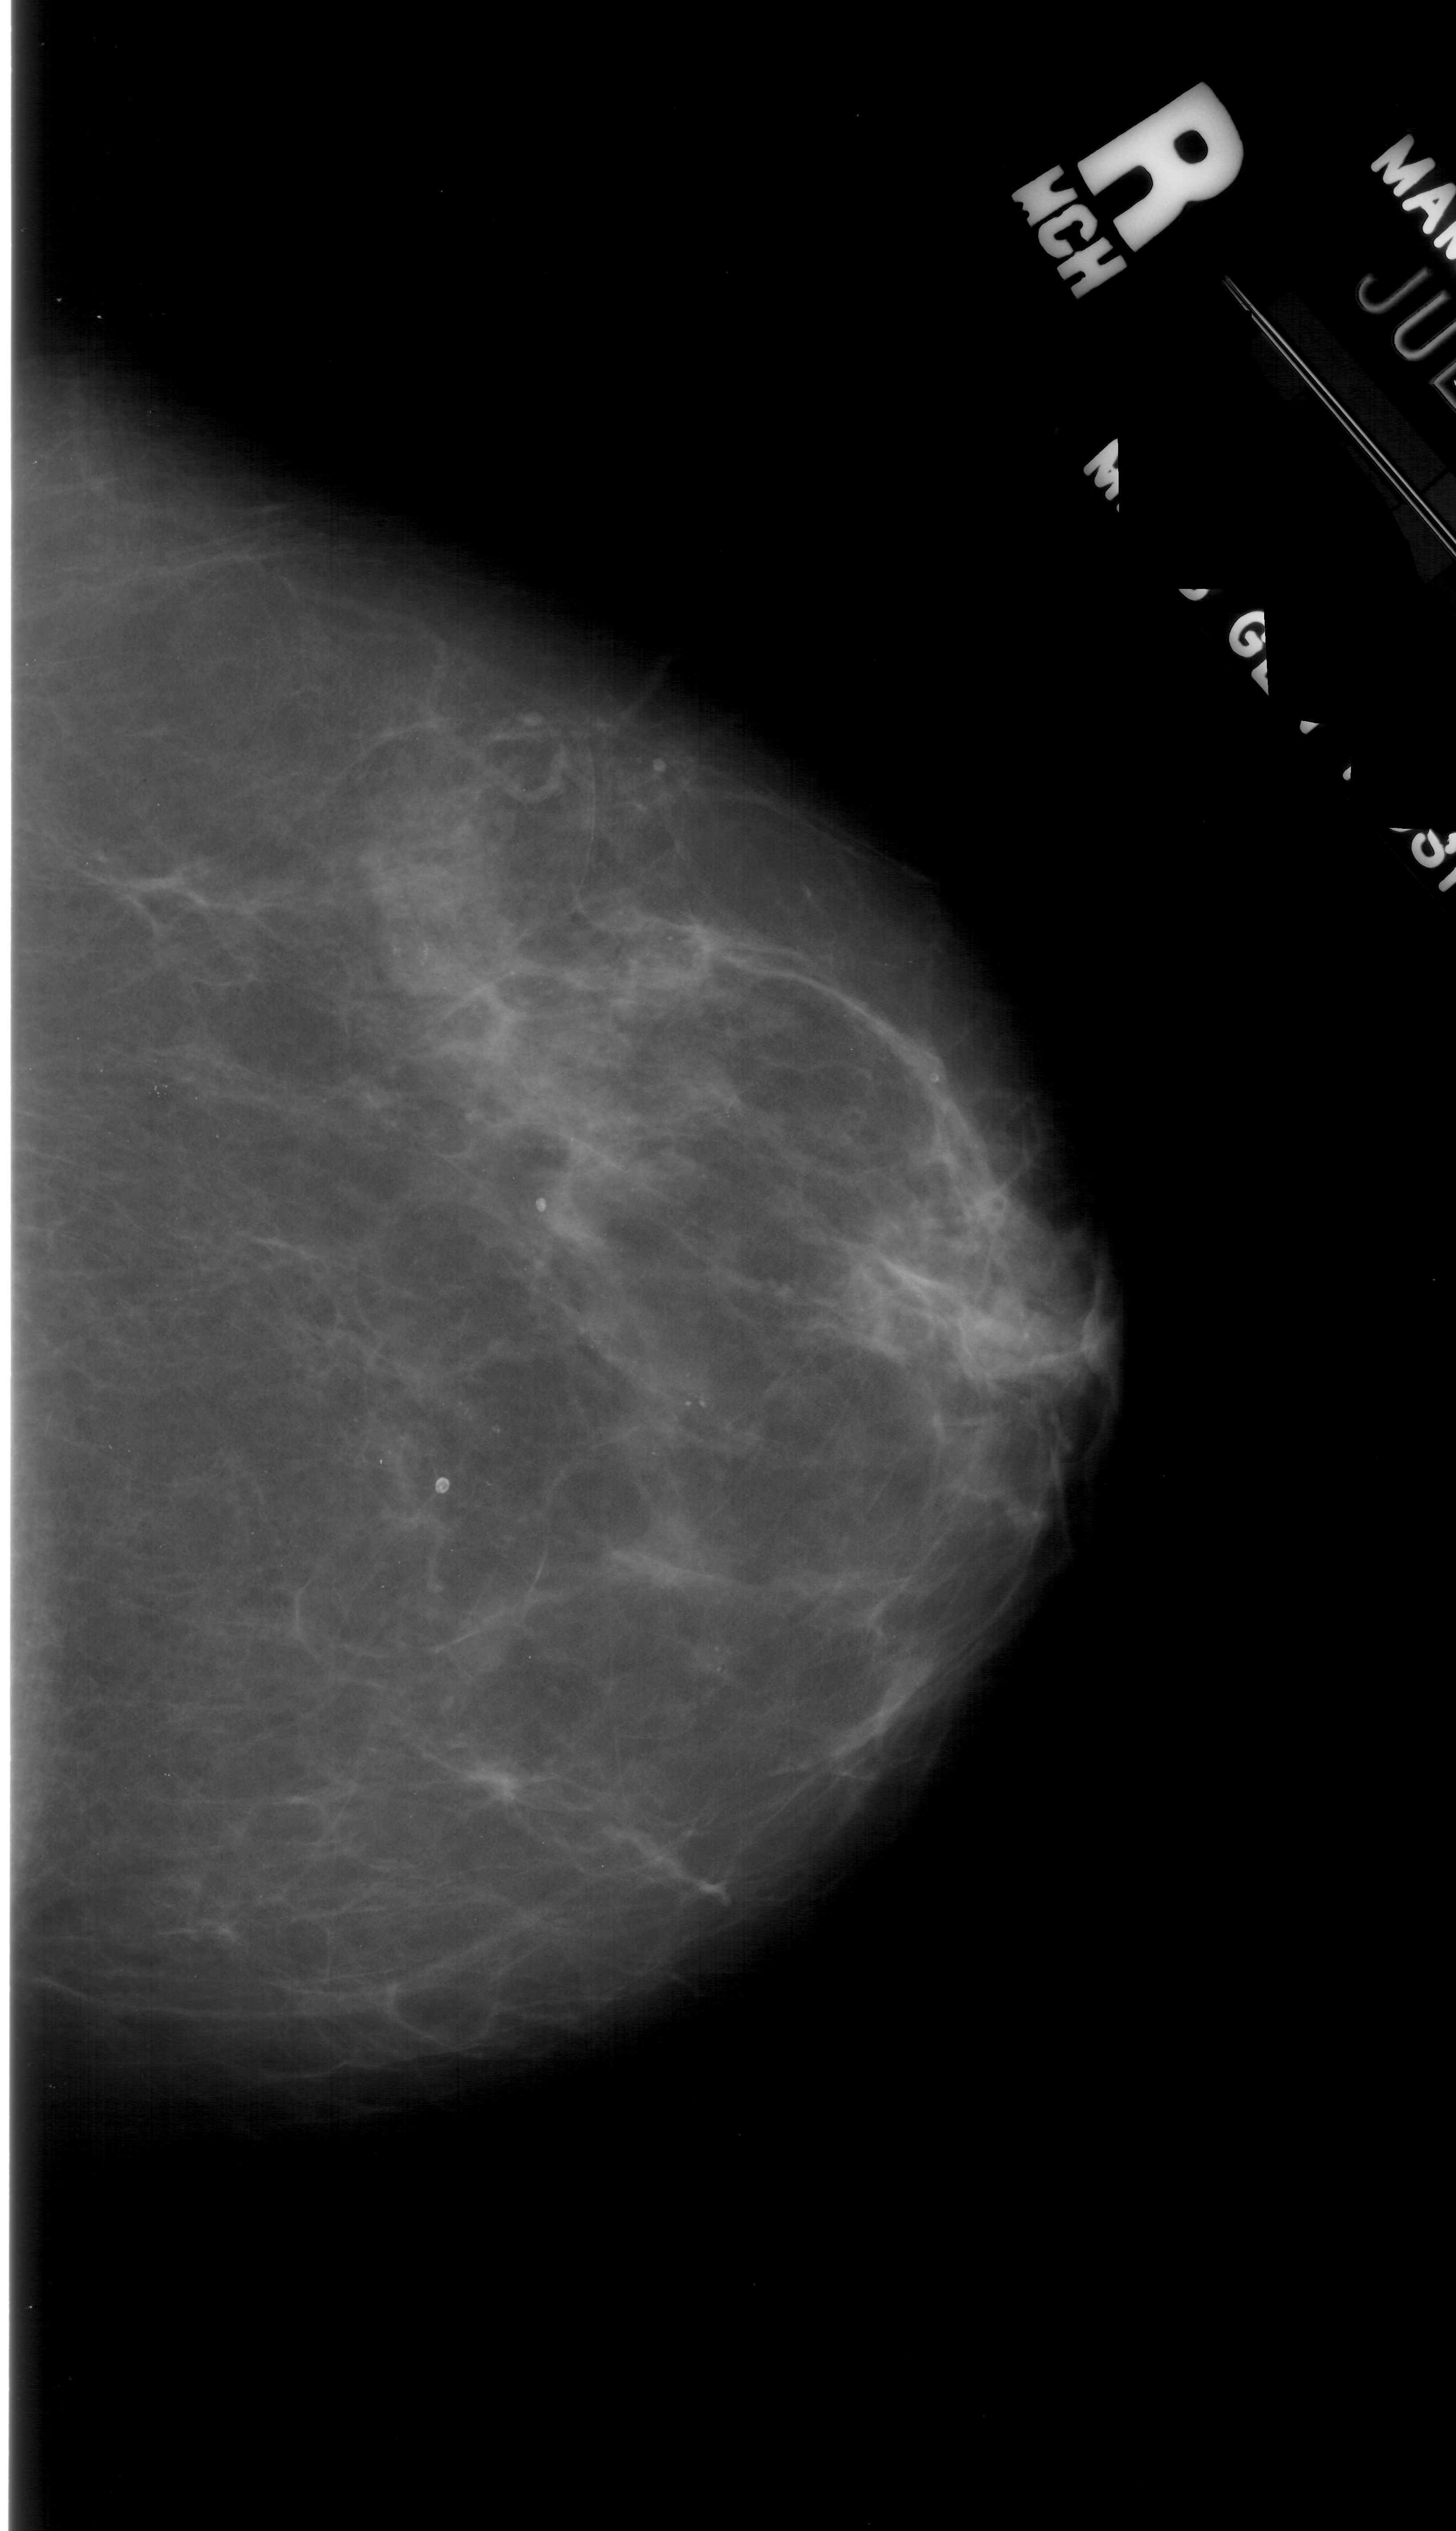
Digitized screen-film mammogram; right breast; CC view; BI-RADS breast density category 2 (scale 1–4).
- Marked abnormality: calcifications, morphology pleomorphic, distribution clustered; BI-RADS assessment category 4; subtlety rating 2 on a 1 (subtle) to 5 (obvious) scale; pathology (as recorded): benign.